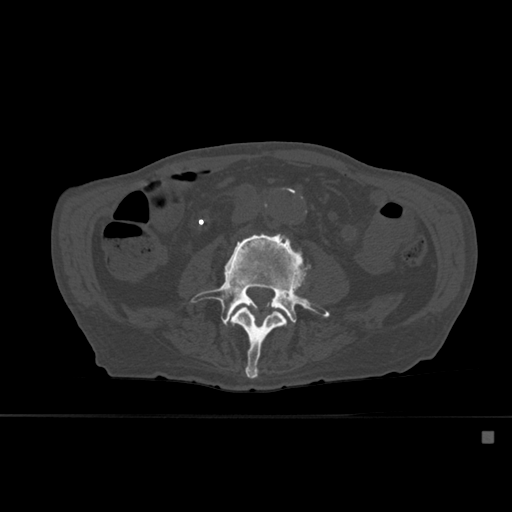
CT including the spine, one axial slice. Slice 202 of 527 in the series (ordered by position). Bone window (W 1800 / L 400 HU). 1.5 mm slice thickness. 512 × 512 image matrix. Male patient, age 78 years. Case-level facts recorded for this patient, not image findings: primary cancer: prostate.
Annotated regions visible in this slice (semi-automatic segmentation, software-assisted and operator-edited):
- L3 vertebra: bounding box (x1, y1, x2, y2) in pixels: (224, 307, 287, 379)
- L4 vertebra: (190, 233, 330, 324)